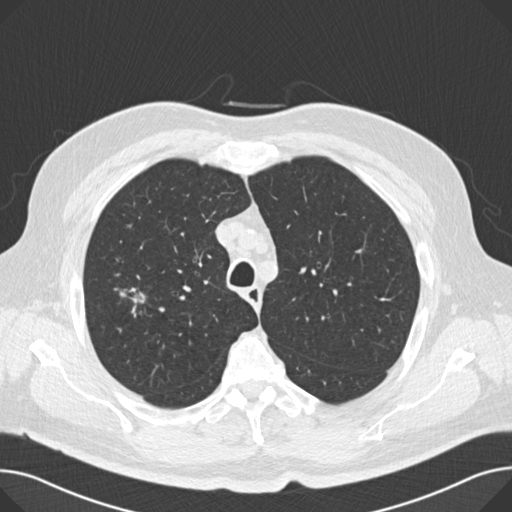
Axial slice from a low-dose chest CT screening exam, second screening round (one year after baseline), lung window (W 1500 / L -600 HU), 2 mm slice thickness, standard (soft-tissue) reconstruction kernel (B30f). Male participant, aged 67 years at enrolment. Current smoker at enrolment.
Lesion marked by an expert reader, box from (x=125, y=285) to (x=151, y=311) px. No non-calcified nodule or mass ≥4 mm was recorded by the screening reader at this exam. Official screen result: negative screen, significant abnormalities not suspicious for lung cancer. Participant outcome: lung cancer diagnosed 194 days after this screen — small cell carcinoma, NOS, right middle lobe, stage IA (AJCC 6th edition), 20 mm at pathology.